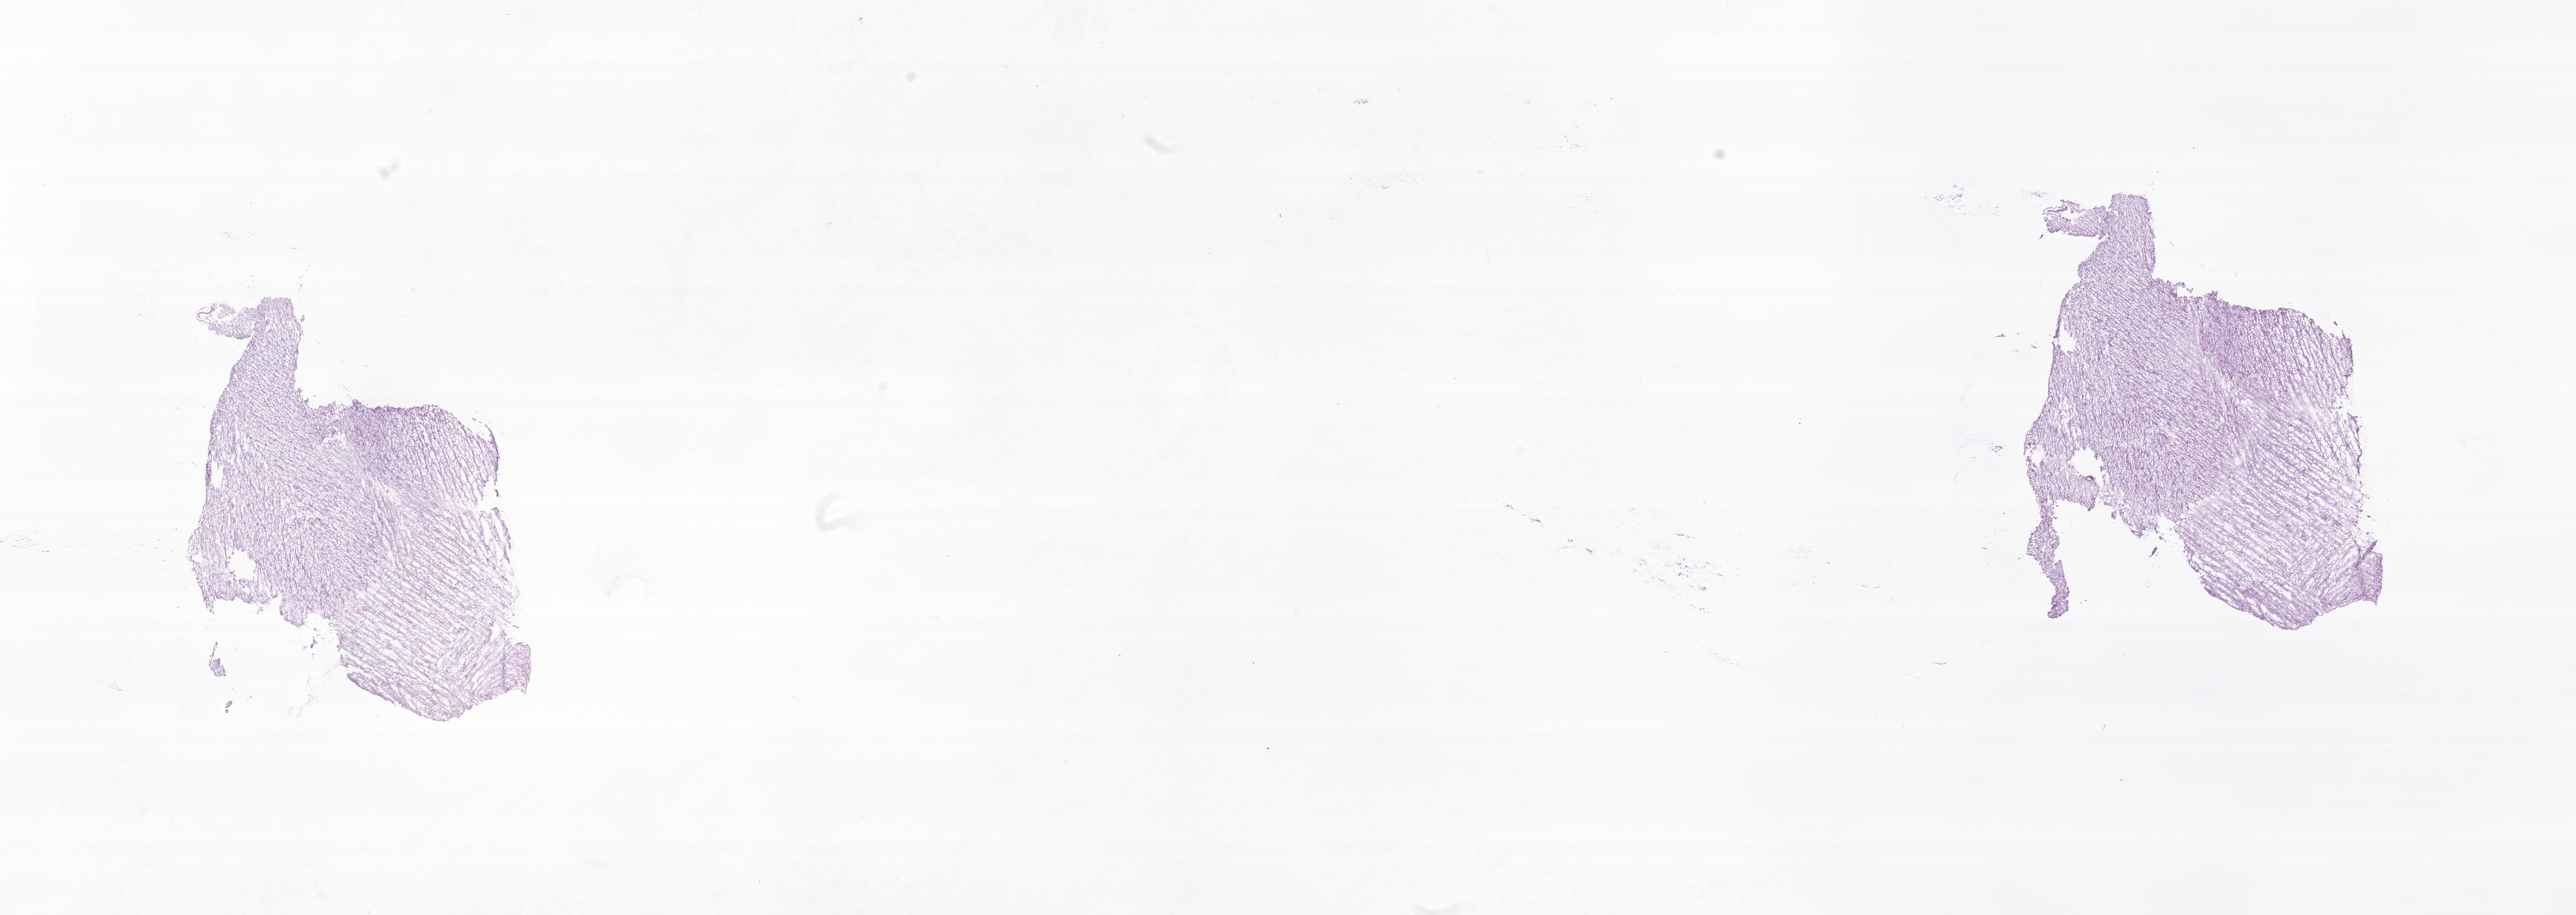
Haematoxylin and eosin whole-slide image of tumor tissue from the brain, whole scanned area (about 24.7 x 8.8 mm) shown as a low-resolution overview; cryosection (OCT / tissue freezing medium). Female patient, age 182 months (15 years 2 months).
Recorded diagnosis: Pilocytic astrocytoma.